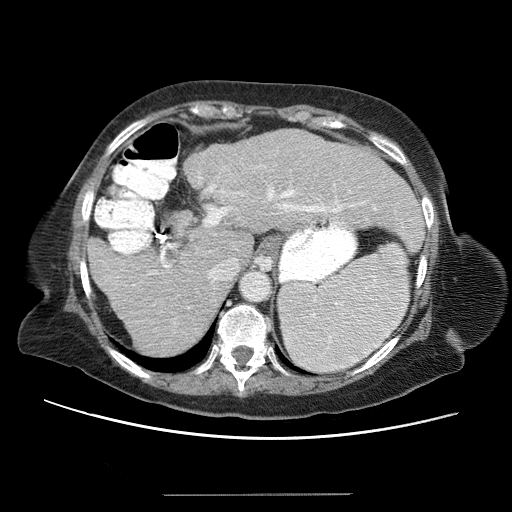
Contrast-enhanced abdominal CT (liver protocol), one axial slice. Slice 43 of 65 in the series (ordered by position). Reconstruction kernel STANDARD. 120 kVp. Soft-tissue window (W 400 / L 40 HU). 2.5 mm slice thickness. 512 × 512 image matrix, field of view 380 × 380 mm. Case-level facts recorded for this patient, not image findings: diagnosis: hepatocellular carcinoma (patient treated with transarterial chemoembolisation; whether this scan precedes or follows treatment is not stated here); TNM stage (as recorded): Stage-IIIB; Child-Pugh class: A; tumour differentiation: moderately differentiated; tumour nodularity: uninodular.
Outlined on this slice (semi-automatic segmentation, software-assisted and operator-edited):
- liver parenchyma outside the tumour (the mass and vessels are separate outlines, so this box may not span the whole liver): bounding box [x1, y1, x2, y2] px = [90, 130, 422, 352]
- liver vessels: [92, 154, 409, 334]